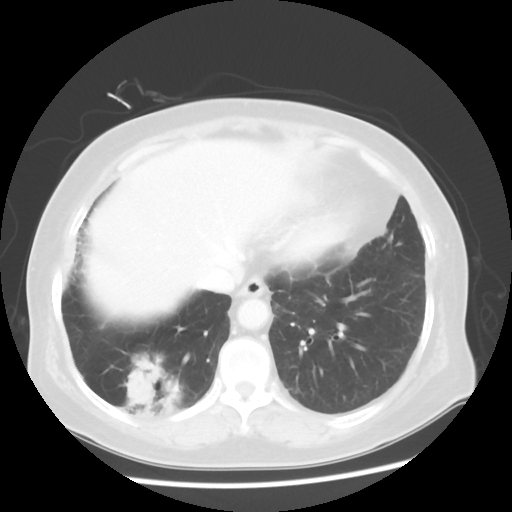
Chest CT, one axial slice. Position 16 of 56 along the scan axis. Reconstruction kernel STANDARD. 120 kVp. Lung window (W 1500 / L -600 HU). 5 mm slice thickness. 512 × 512 image matrix, field of view 360 × 360 mm. Patient: female, 64 years. From the clinical record (not read from this slice): clinical TNM (as recorded): Tis N0 M0.
Annotated regions visible in this slice (bounding box drawn by a radiologist):
- lung tumour (recorded histology: adenocarcinoma): box from (x=113, y=342) to (x=192, y=427) px